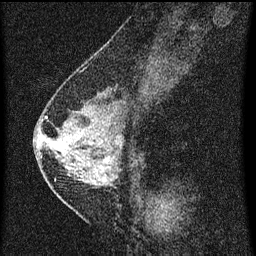
Breast MRI (dynamic contrast-enhanced), one sagittal slice; slice 27 of 60 in the series (ordered by position); dynamic contrast-enhanced series, image 2 of 3 at this slice position (ordered by acquisition); 1.5 T; TE 4.2 ms, TR 8 ms; 2 mm slice thickness; 256 × 256 image matrix, field of view 180 × 180 mm. Patient: female, 47 years.
Outlined on this slice (semi-automatic segmentation, software-assisted and operator-edited):
- analysis volume of interest (the breast-tissue region the enhancement analysis was run in; not a lesion): box from (x=42, y=92) to (x=139, y=199) px
- tumour enhancement mask (voxels above the 70 % enhancement threshold inside the analysis volume of interest): (x=46, y=118)–(x=122, y=171)